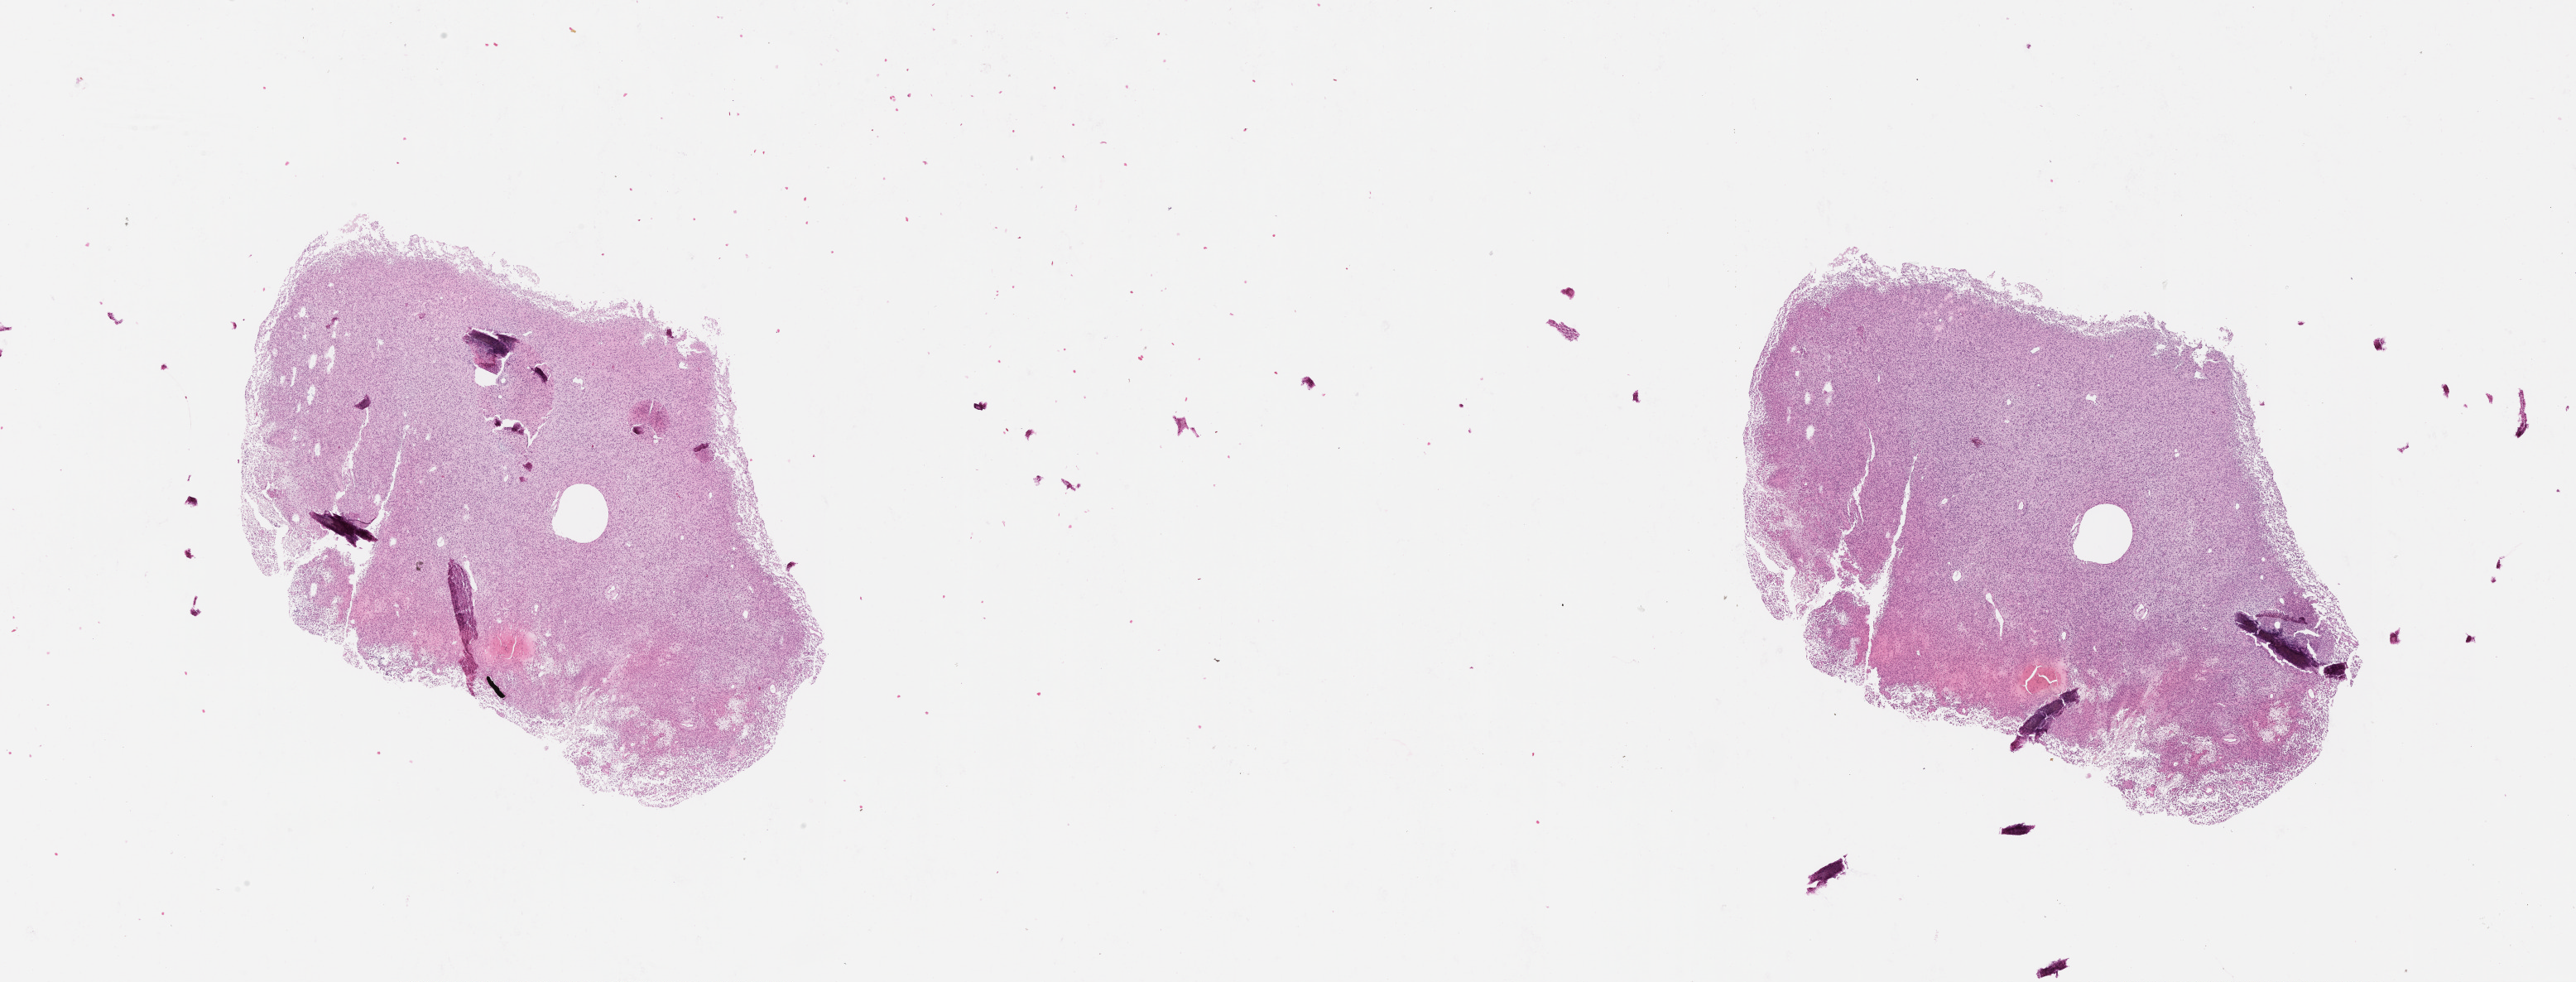
Digitized H&E tissue section (whole slide), shown as a low-resolution overview of the whole scanned area (about 25.1 x 9.5 mm, slide scanned at 20x); tumour tissue sample, sampled site: brain. Patient: female, age 54 years. Pathologist review of this section (percent, as recorded): tumour nuclei 80%, necrosis 15%.
Histologic diagnosis: Glioblastoma. Primary tumour site (as recorded): temporal lobe.